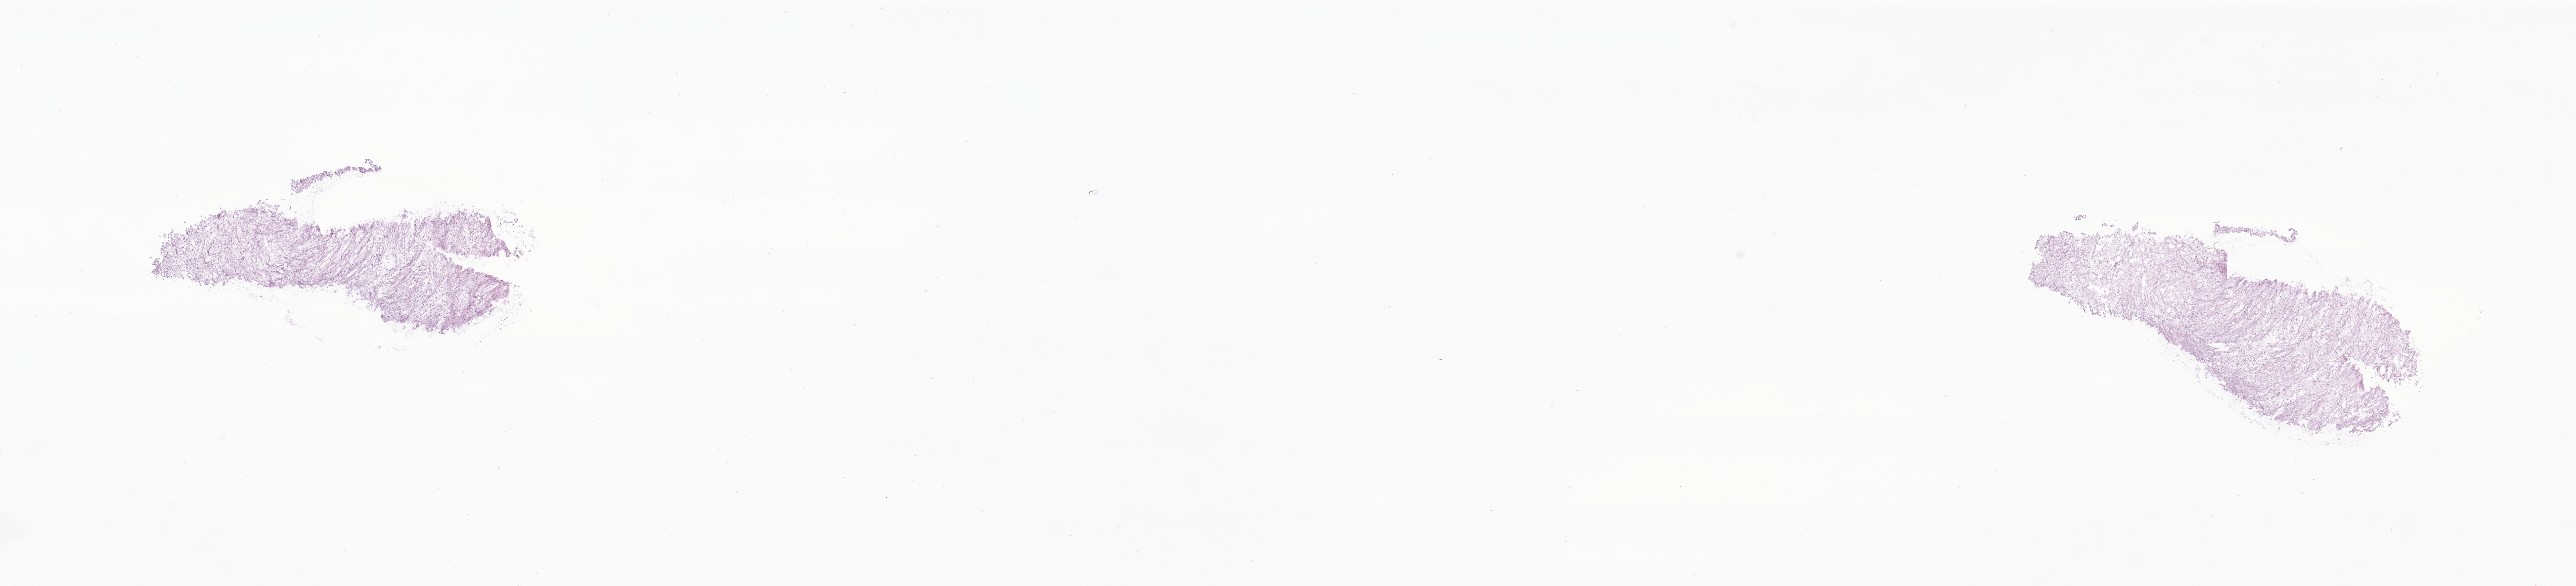
Digitized haematoxylin and eosin-stained section of tumor tissue from the breast — whole scanned area (about 32.4 x 7.4 mm) shown as a low-resolution overview. Frozen section. Patient female; age 213 months (17 years 9 months).
• diagnosis: Sarcoma, NOS